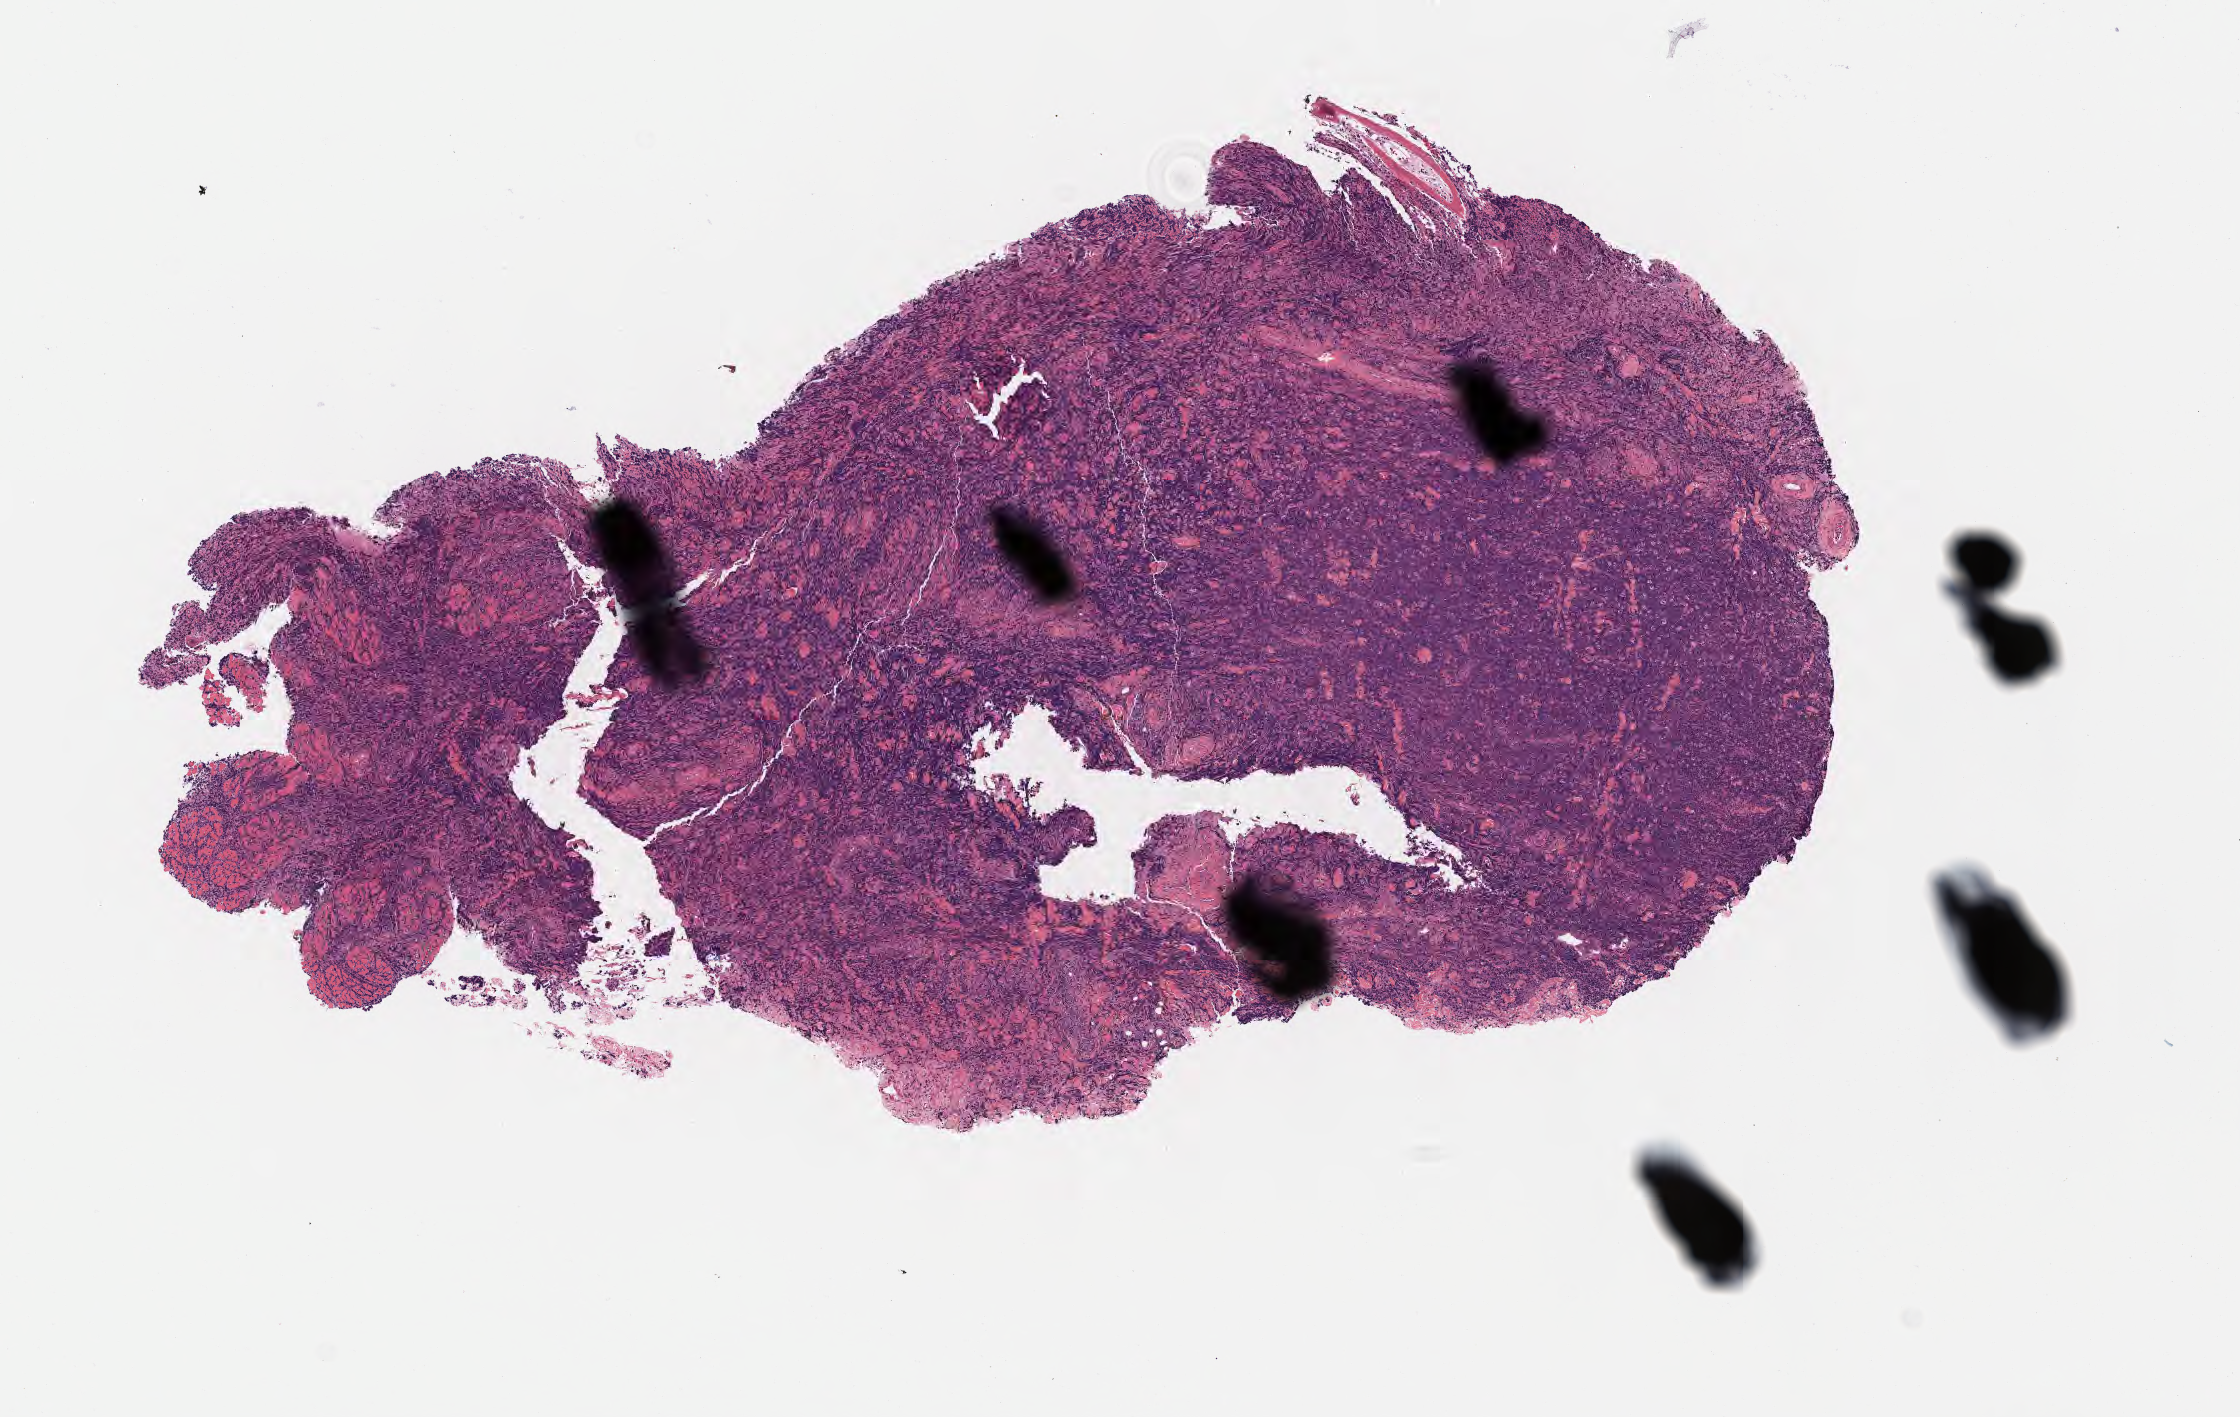
Whole-slide image, hematoxylin and eosin (H&E) stain — shown as a low-resolution overview of the whole scanned area (about 9.1 x 5.7 mm), specimen: tumor tissue, anatomic site: lip. Male, age 7 years at initial diagnosis.
Histologic diagnosis: Diffuse large B-cell lymphoma, NOS.